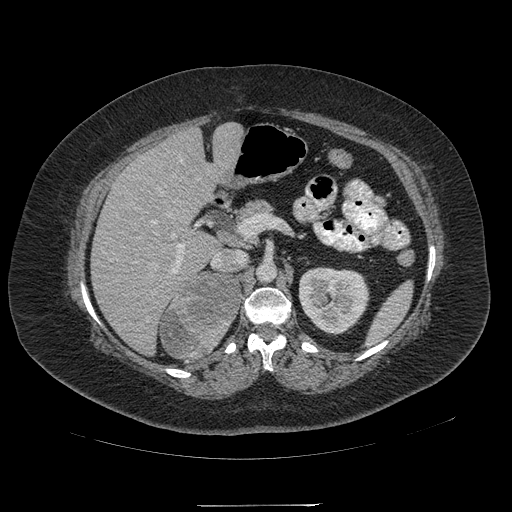
Contrast-enhanced abdominal CT, one axial slice. Slice 123 of 217 in the series (ordered by position). Reconstruction kernel STANDARD. 120 kVp. Intravenous contrast given. Soft-tissue window (W 400 / L 40 HU). 1.25 mm slice thickness. 512 × 512 image matrix, field of view 453 × 453 mm. Patient: female, 55 years. From the clinical record (not read from this slice): diagnosis: adrenocortical carcinoma; tumour side: right adrenal; tumour size at pathology: 11 cm.
Structures marked on this image (semi-automatic segmentation, software-assisted and operator-edited):
- mass: bounding box (x1, y1, x2, y2) in pixels: (161, 273, 241, 358)